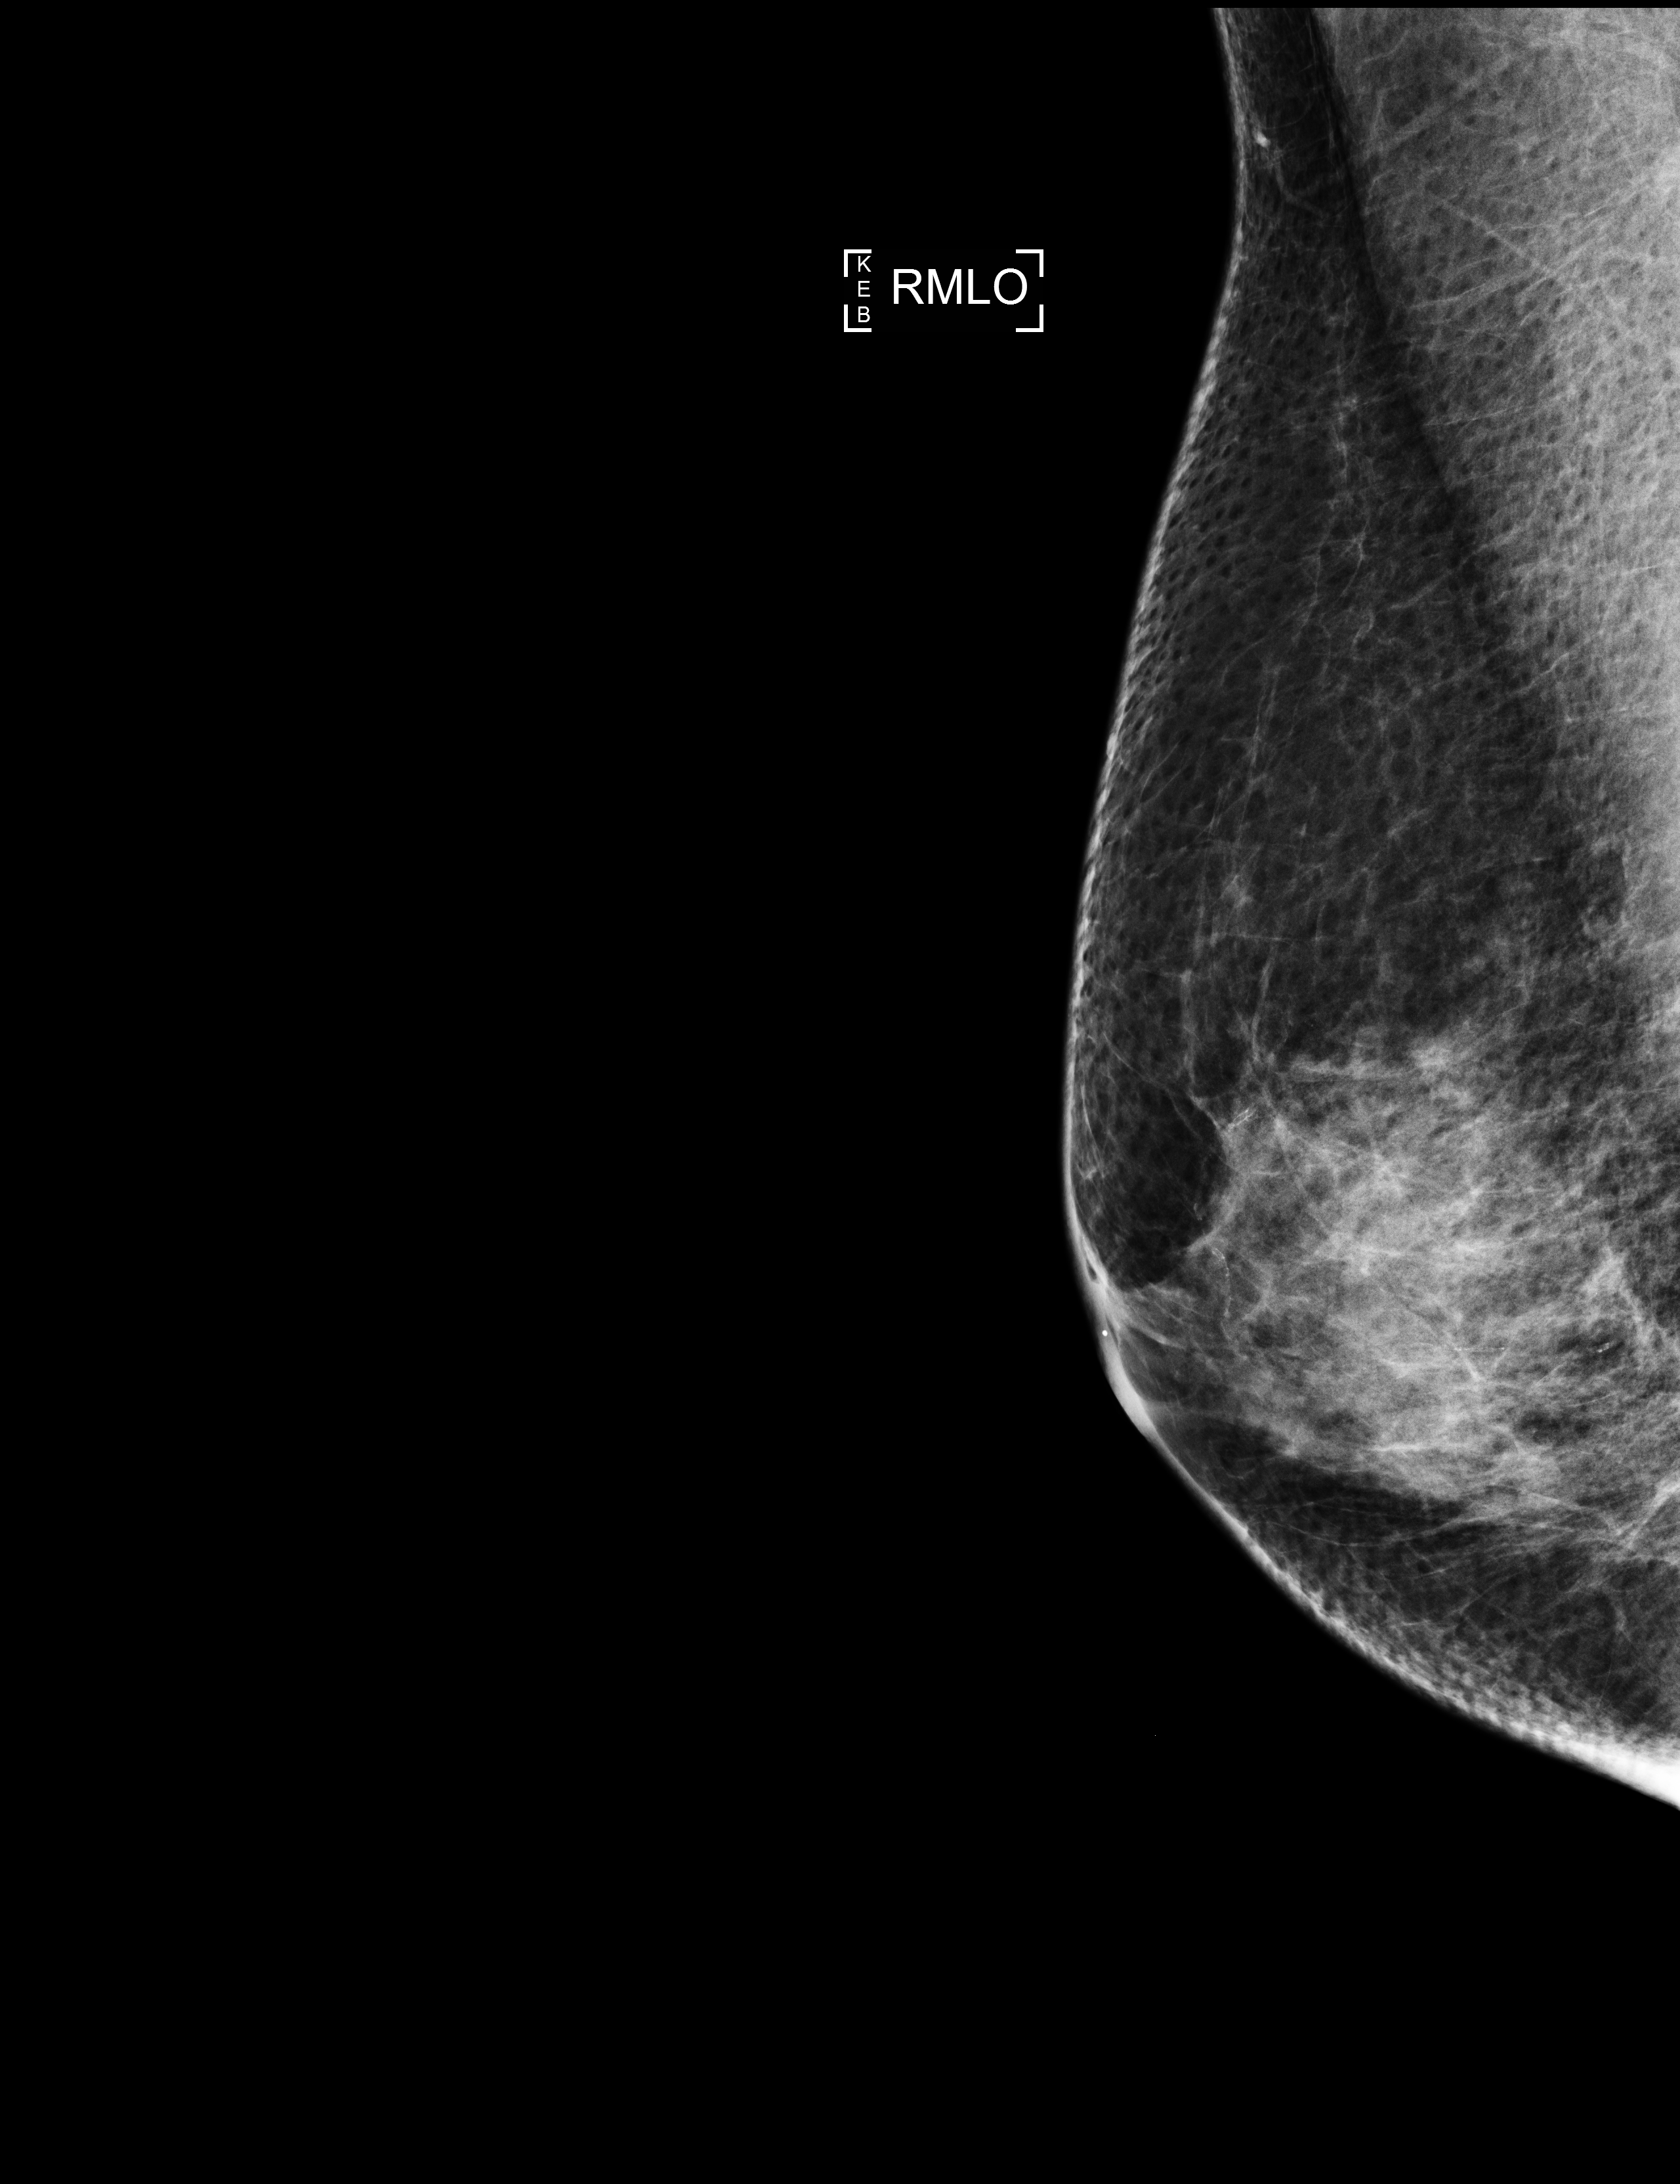
Digital mammogram (FFDM); right breast; MLO view; annual screening mammography examination; system: Selenia Dimensions. Patient aged 64 years (female).
Breast density at the screening exam (both breasts): extremely dense (BI-RADS density category d). Final BI-RADS assessment for this screening round (tomosynthesis exam, both breasts): category 1. Recall: no recall after this screen.